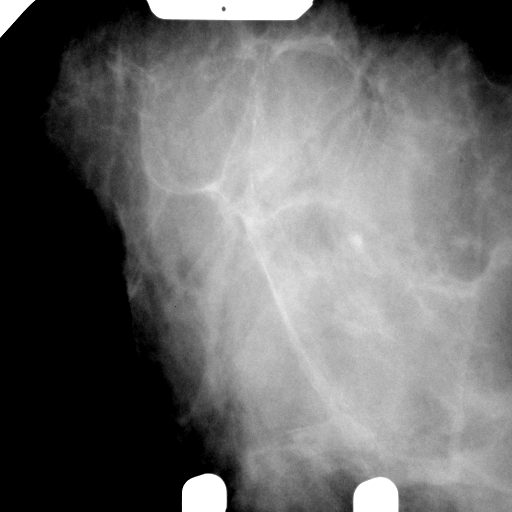
Spot-compression mammographic view.
Pathology recorded for this patient (not read from this image): pathology diagnosis: benign fibroadenoma (right breast); pathology report notes: RIGHT BREAST CALCIFICATION WITH NEEDLE LOCATION: FIBROADENOMA (1.9CM). REMAINING BREAST TISSUE WITH ADENOSIS, FOCAL FIBROADENOMATOUS CHANGES, APOCRINE METAPLASIA, FIBROCYSTIC CHANGES, SMALL INTRADUCTAL PAPILLOMAS, AND USUAL TYPE DUCTAL HYPERPLASIA. MICROCALCIFICATIONS ASSOCIATED WITH BENIGN BREAST TISSUE ARE IDENTIFIED. NO IN-SITU OR INVASIVE CARCINOMA.